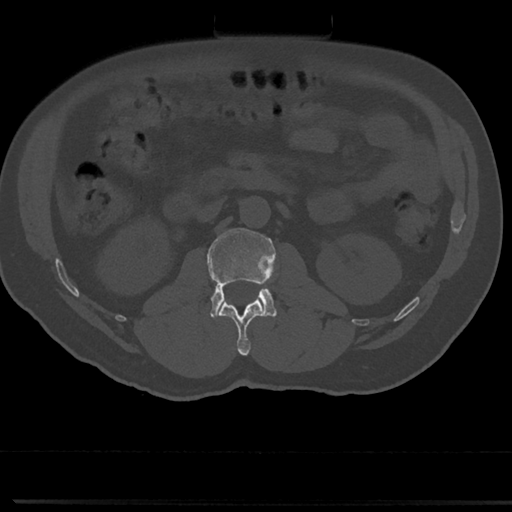
CT including the spine, one axial slice. Slice 41 of 817 in the series (ordered by position). Reconstruction kernel Br40s/3. Bone window (W 1800 / L 400 HU). 512 × 512 image matrix. Patient: male, 61 years. Case-level facts recorded for this patient, not image findings: primary cancer: prostate.
Structures marked on this image (semi-automatically segmented with operator editing):
- L1 vertebra: bounding box <219,299,264,355> (left, top, right, bottom; pixels)
- L2 vertebra: <207,228,276,317>